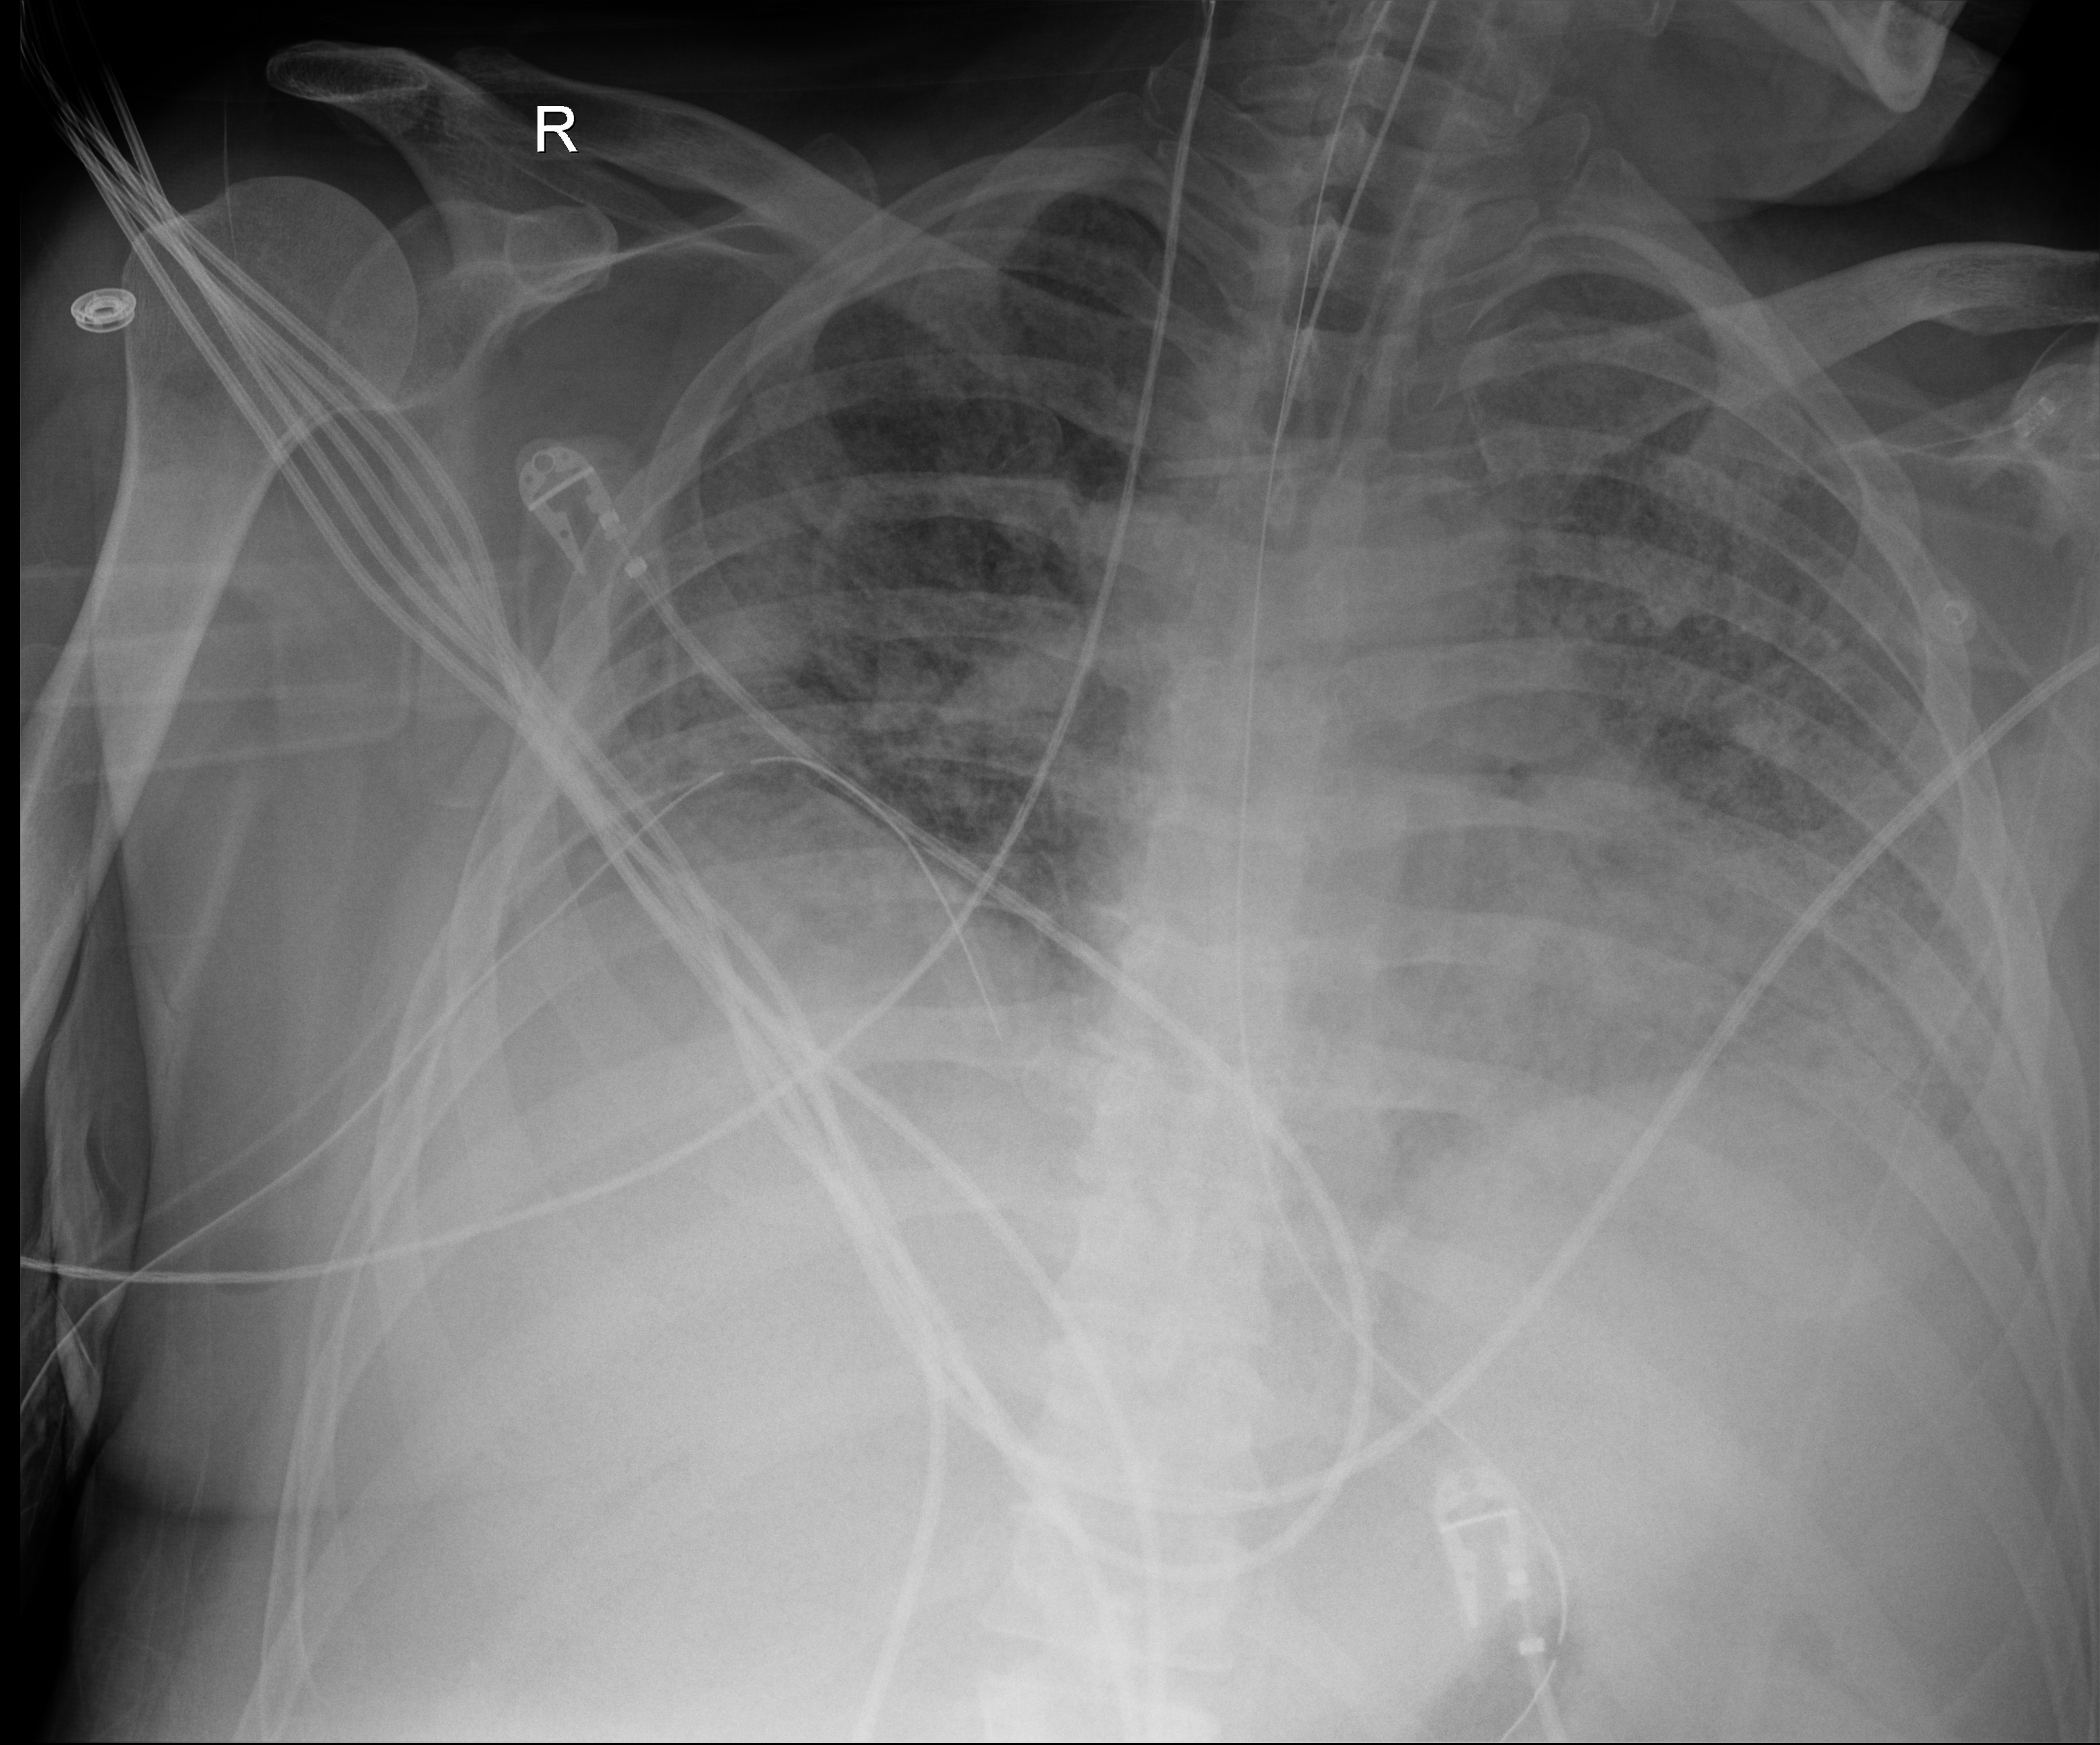
Portable chest radiograph; anteroposterior (AP) projection. Male patient hospitalised with COVID-19, age 18–59 years.
Hospital-stay facts (about this admission, not read from this image; timing relative to this image not recorded):
- other chronic lung disease (admission record): no